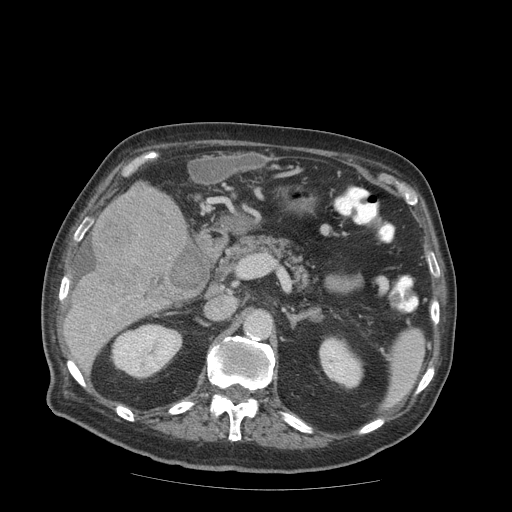
Contrast-enhanced abdominal CT (liver protocol), one axial slice; reconstruction kernel STANDARD; soft-tissue window (W 400 / L 40 HU); 2.5 mm slice thickness; 512 × 512 image matrix, field of view 420 × 420 mm. From the clinical record (not read from this slice): diagnosis: hepatocellular carcinoma (patient treated with transarterial chemoembolisation; whether this scan precedes or follows treatment is not stated here); TNM stage (as recorded): Stage-IIIB; Child-Pugh class: A; tumour differentiation: well differentiated.
Outlined on this slice (semi-automatically segmented with operator editing):
- liver parenchyma outside the tumour (the mass and vessels are separate outlines, so this box may not span the whole liver): bounding box [x1, y1, x2, y2] px = [64, 190, 193, 348]
- mass: [82, 182, 189, 305]
- liver vessels: [92, 325, 95, 330]